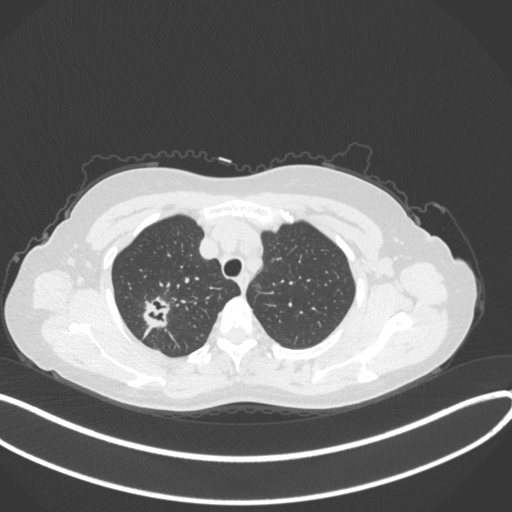
Chest CT, one axial slice; slice 296 of 342 in the series (ordered by position); reconstruction kernel B31f; 120 kVp; lung window (W 1500 / L -600 HU); 1 mm slice thickness; 512 × 512 image matrix, field of view 400 × 400 mm. Female patient, age 50 years. From the clinical record (not read from this slice): clinical TNM (as recorded): T1c N0 M0; histopathological grade: G2-3.
Annotated regions visible in this slice (bounding box drawn by a radiologist):
- lung tumour (recorded histology: adenocarcinoma): bounding box [x1, y1, x2, y2] px = [137, 293, 170, 336]